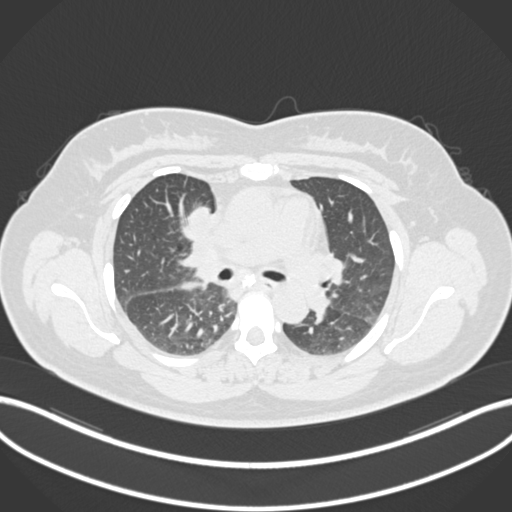
Chest CT, one axial slice. Slice 107 of 183 in the series (ordered by position). Reconstruction kernel B30f. Lung window (W 1500 / L -600 HU). 1 mm slice thickness. 512 × 512 image matrix, field of view 400 × 400 mm. Patient: female, 46 years. From the clinical record (not read from this slice): clinical TNM (as recorded): T2a N1 M0.
Structures marked on this image (rectangle marked by the reading radiologist):
- lung tumour (recorded histology: adenocarcinoma): bounding box [x1, y1, x2, y2] px = [182, 198, 212, 236]